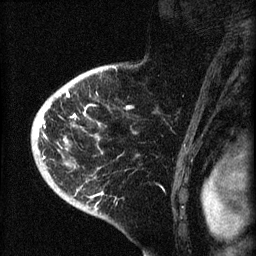
Breast MRI (dynamic contrast-enhanced), one sagittal slice. Position 51 of 60 along the scan axis. Dynamic contrast-enhanced series, image 2 of 4 at this slice position (ordered by acquisition). 1.5 T. TE 4.2 ms, TR 8.2 ms. 2 mm slice thickness. 256 × 256 image matrix. Female patient, age 71 years.
Structures marked on this image (semi-automatically segmented with operator editing):
- analysis volume of interest (the breast-tissue region the enhancement analysis was run in; not a lesion): bounding box <35,75,137,190> (left, top, right, bottom; pixels)
- tumour enhancement mask (voxels above the 70 % enhancement threshold inside the analysis volume of interest): <35,90,99,159>